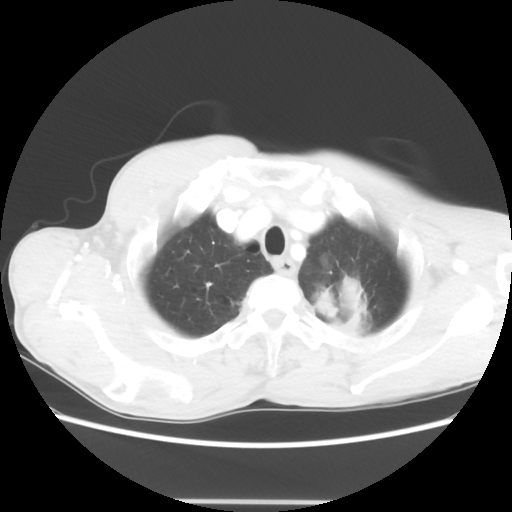
Chest CT, one axial slice. Slice 57 of 62 in the series (ordered by position). Reconstruction kernel STANDARD. 100 kVp. Lung window (W 1500 / L -600 HU). 5 mm slice thickness. 512 × 512 image matrix. Male patient, age 61 years. From the clinical record (not read from this slice): clinical TNM (as recorded): T3 N1 M1.
Annotated regions visible in this slice (bounding box drawn by a radiologist):
- lung tumour (recorded histology: adenocarcinoma): box from (x=314, y=268) to (x=370, y=333) px